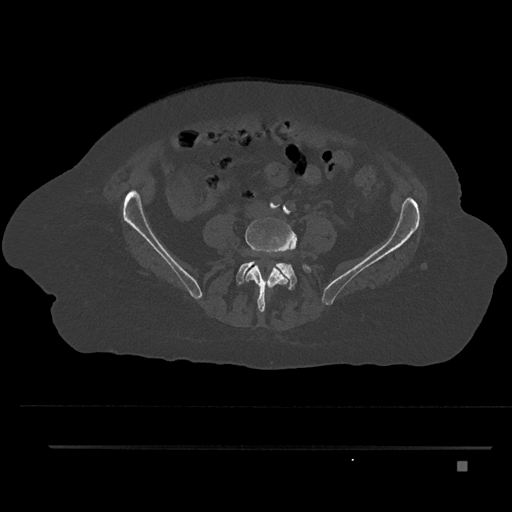
CT including the spine, one axial slice. Slice 63 of 797 in the series (ordered by position). Reconstruction kernel Br40s/3. 120 kVp. Bone window (W 1800 / L 400 HU). 0.5 mm slice thickness. 512 × 512 image matrix. Patient: female, 76 years. From the clinical record (not read from this slice): primary cancer: lung; vertebrae with lytic lesions (as recorded): T11, L3.
Annotated regions visible in this slice (semi-automatic segmentation, software-assisted and operator-edited):
- L4 vertebra: bounding box (x1, y1, x2, y2) in pixels: (245, 217, 297, 313)
- L5 vertebra: (236, 249, 311, 290)